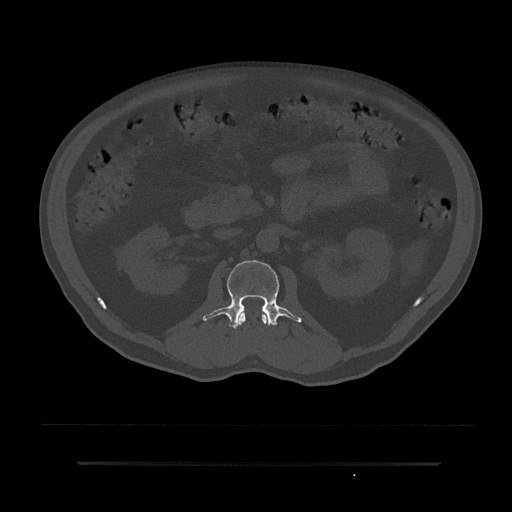
CT including the spine, one axial slice. Position 90 of 797 along the scan axis. Reconstruction kernel Br40s/3. 120 kVp. Bone window (W 1800 / L 400 HU). 0.5 mm slice thickness. 512 × 512 image matrix. Male patient, age 59 years. From the clinical record (not read from this slice): primary cancer: bile ducts; vertebrae with lytic lesions (as recorded): T10.
Outlined on this slice (semi-automatic segmentation, software-assisted and operator-edited):
- L1 vertebra: bounding box (x1, y1, x2, y2) in pixels: (238, 311, 267, 325)
- L2 vertebra: (203, 260, 302, 328)